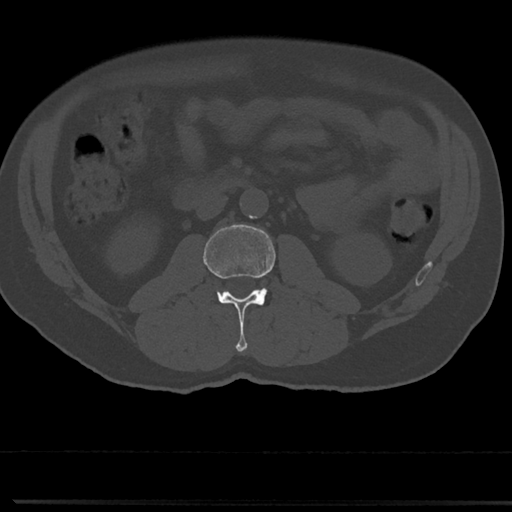
CT including the spine, one axial slice; position 4 of 817 along the scan axis; 120 kVp; bone window (W 1800 / L 400 HU); 0.5 mm slice thickness; 512 × 512 image matrix, field of view 355 × 355 mm. Male patient, age 61 years. Case-level facts recorded for this patient, not image findings: primary cancer: prostate.
Annotated regions visible in this slice (semi-automatically segmented with operator editing):
- L2 vertebra: bounding box (x1, y1, x2, y2) in pixels: (204, 225, 275, 351)